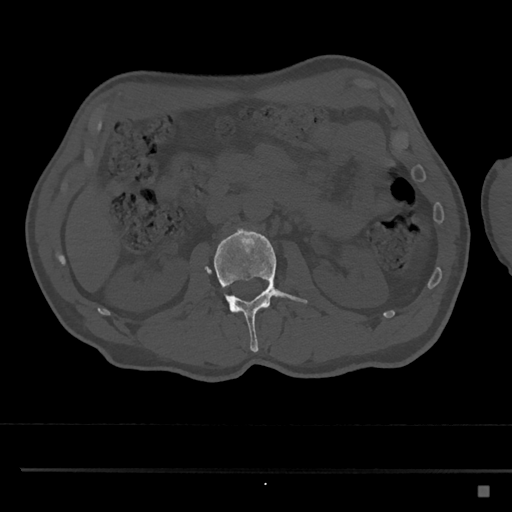
CT including the spine, one axial slice; slice 754 of 797 in the series (ordered by position); bone window (W 1800 / L 400 HU); 0.5 mm slice thickness; 512 × 512 image matrix, field of view 391 × 391 mm. Patient: male, 59 years. Case-level facts recorded for this patient, not image findings: primary cancer: prostate.
Annotated regions visible in this slice (semi-automatic segmentation, software-assisted and operator-edited):
- L2 vertebra: bounding box (x1, y1, x2, y2) in pixels: (204, 227, 307, 352)